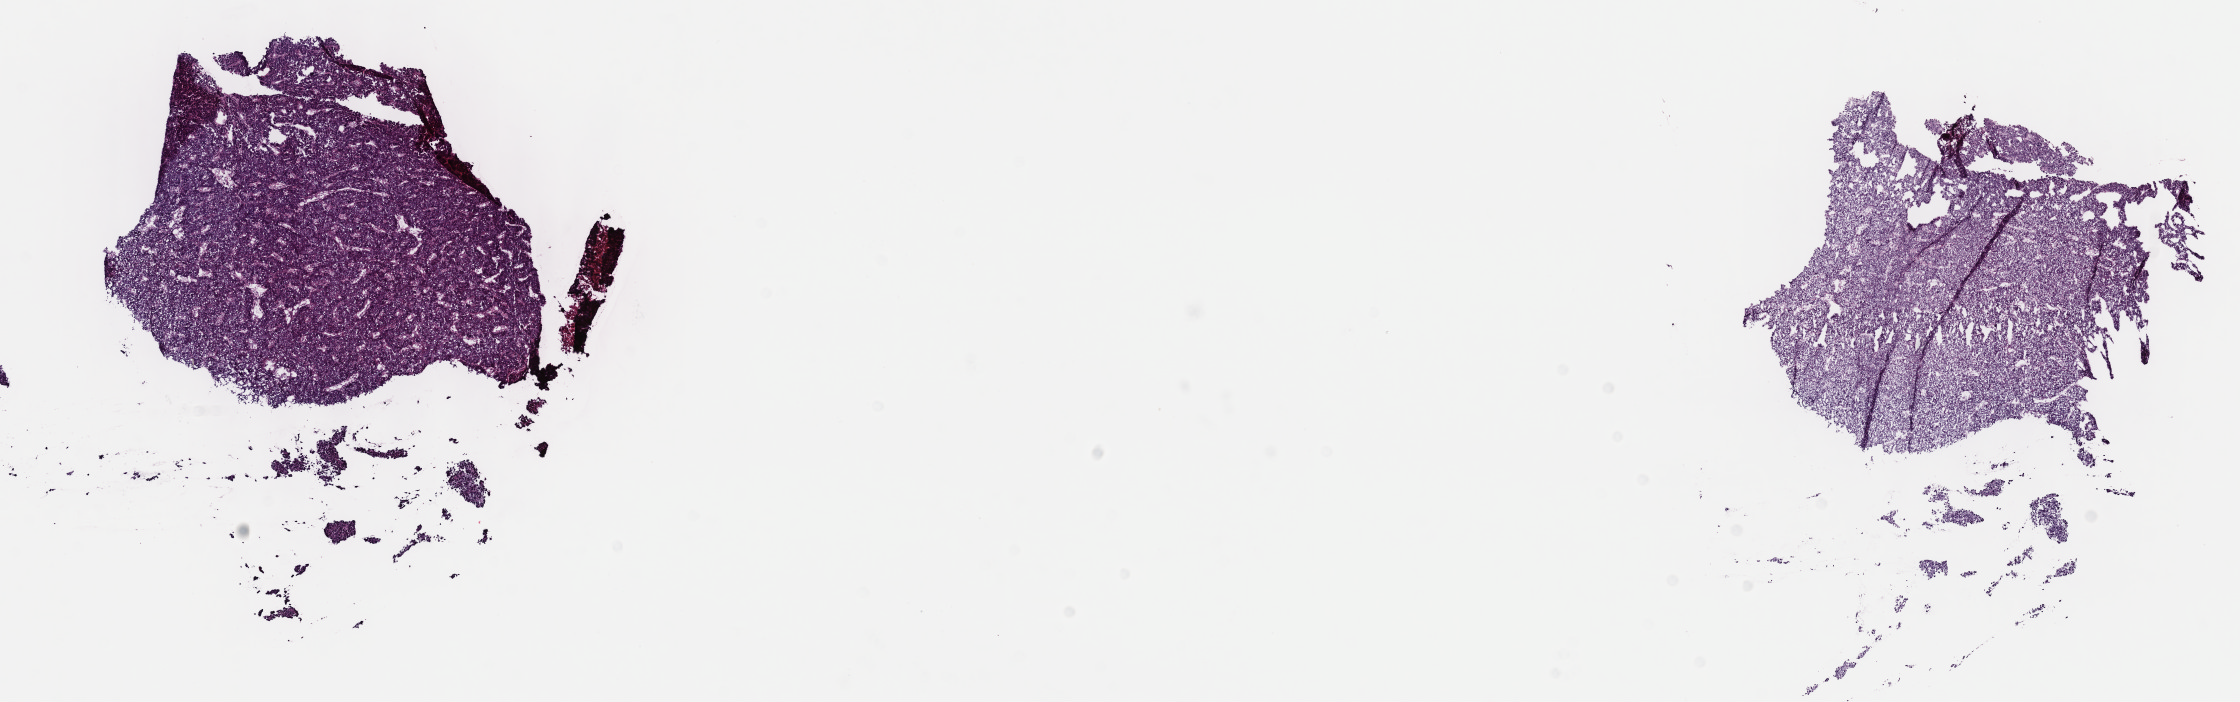
H&E-stained whole-slide image — whole scanned area (about 18.1 x 5.7 mm) shown as a low-resolution overview; frozen section from the top of the tissue portion; primary tumour sample from the liver. Male, age 46 years at initial diagnosis. Histologic grade: G2 (moderately differentiated). Slide review estimates, as recorded: tumour cells 80%, tumour nuclei 80%, normal cells 0%, stromal cells 20%, necrosis 0%. Infiltration values recorded for this section: lymphocyte infiltration 2%, monocyte infiltration 1%, neutrophil infiltration 3%.
• pathologic diagnosis: Hepatocellular carcinoma, NOS
• AJCC pathologic stage: II (6th edition)